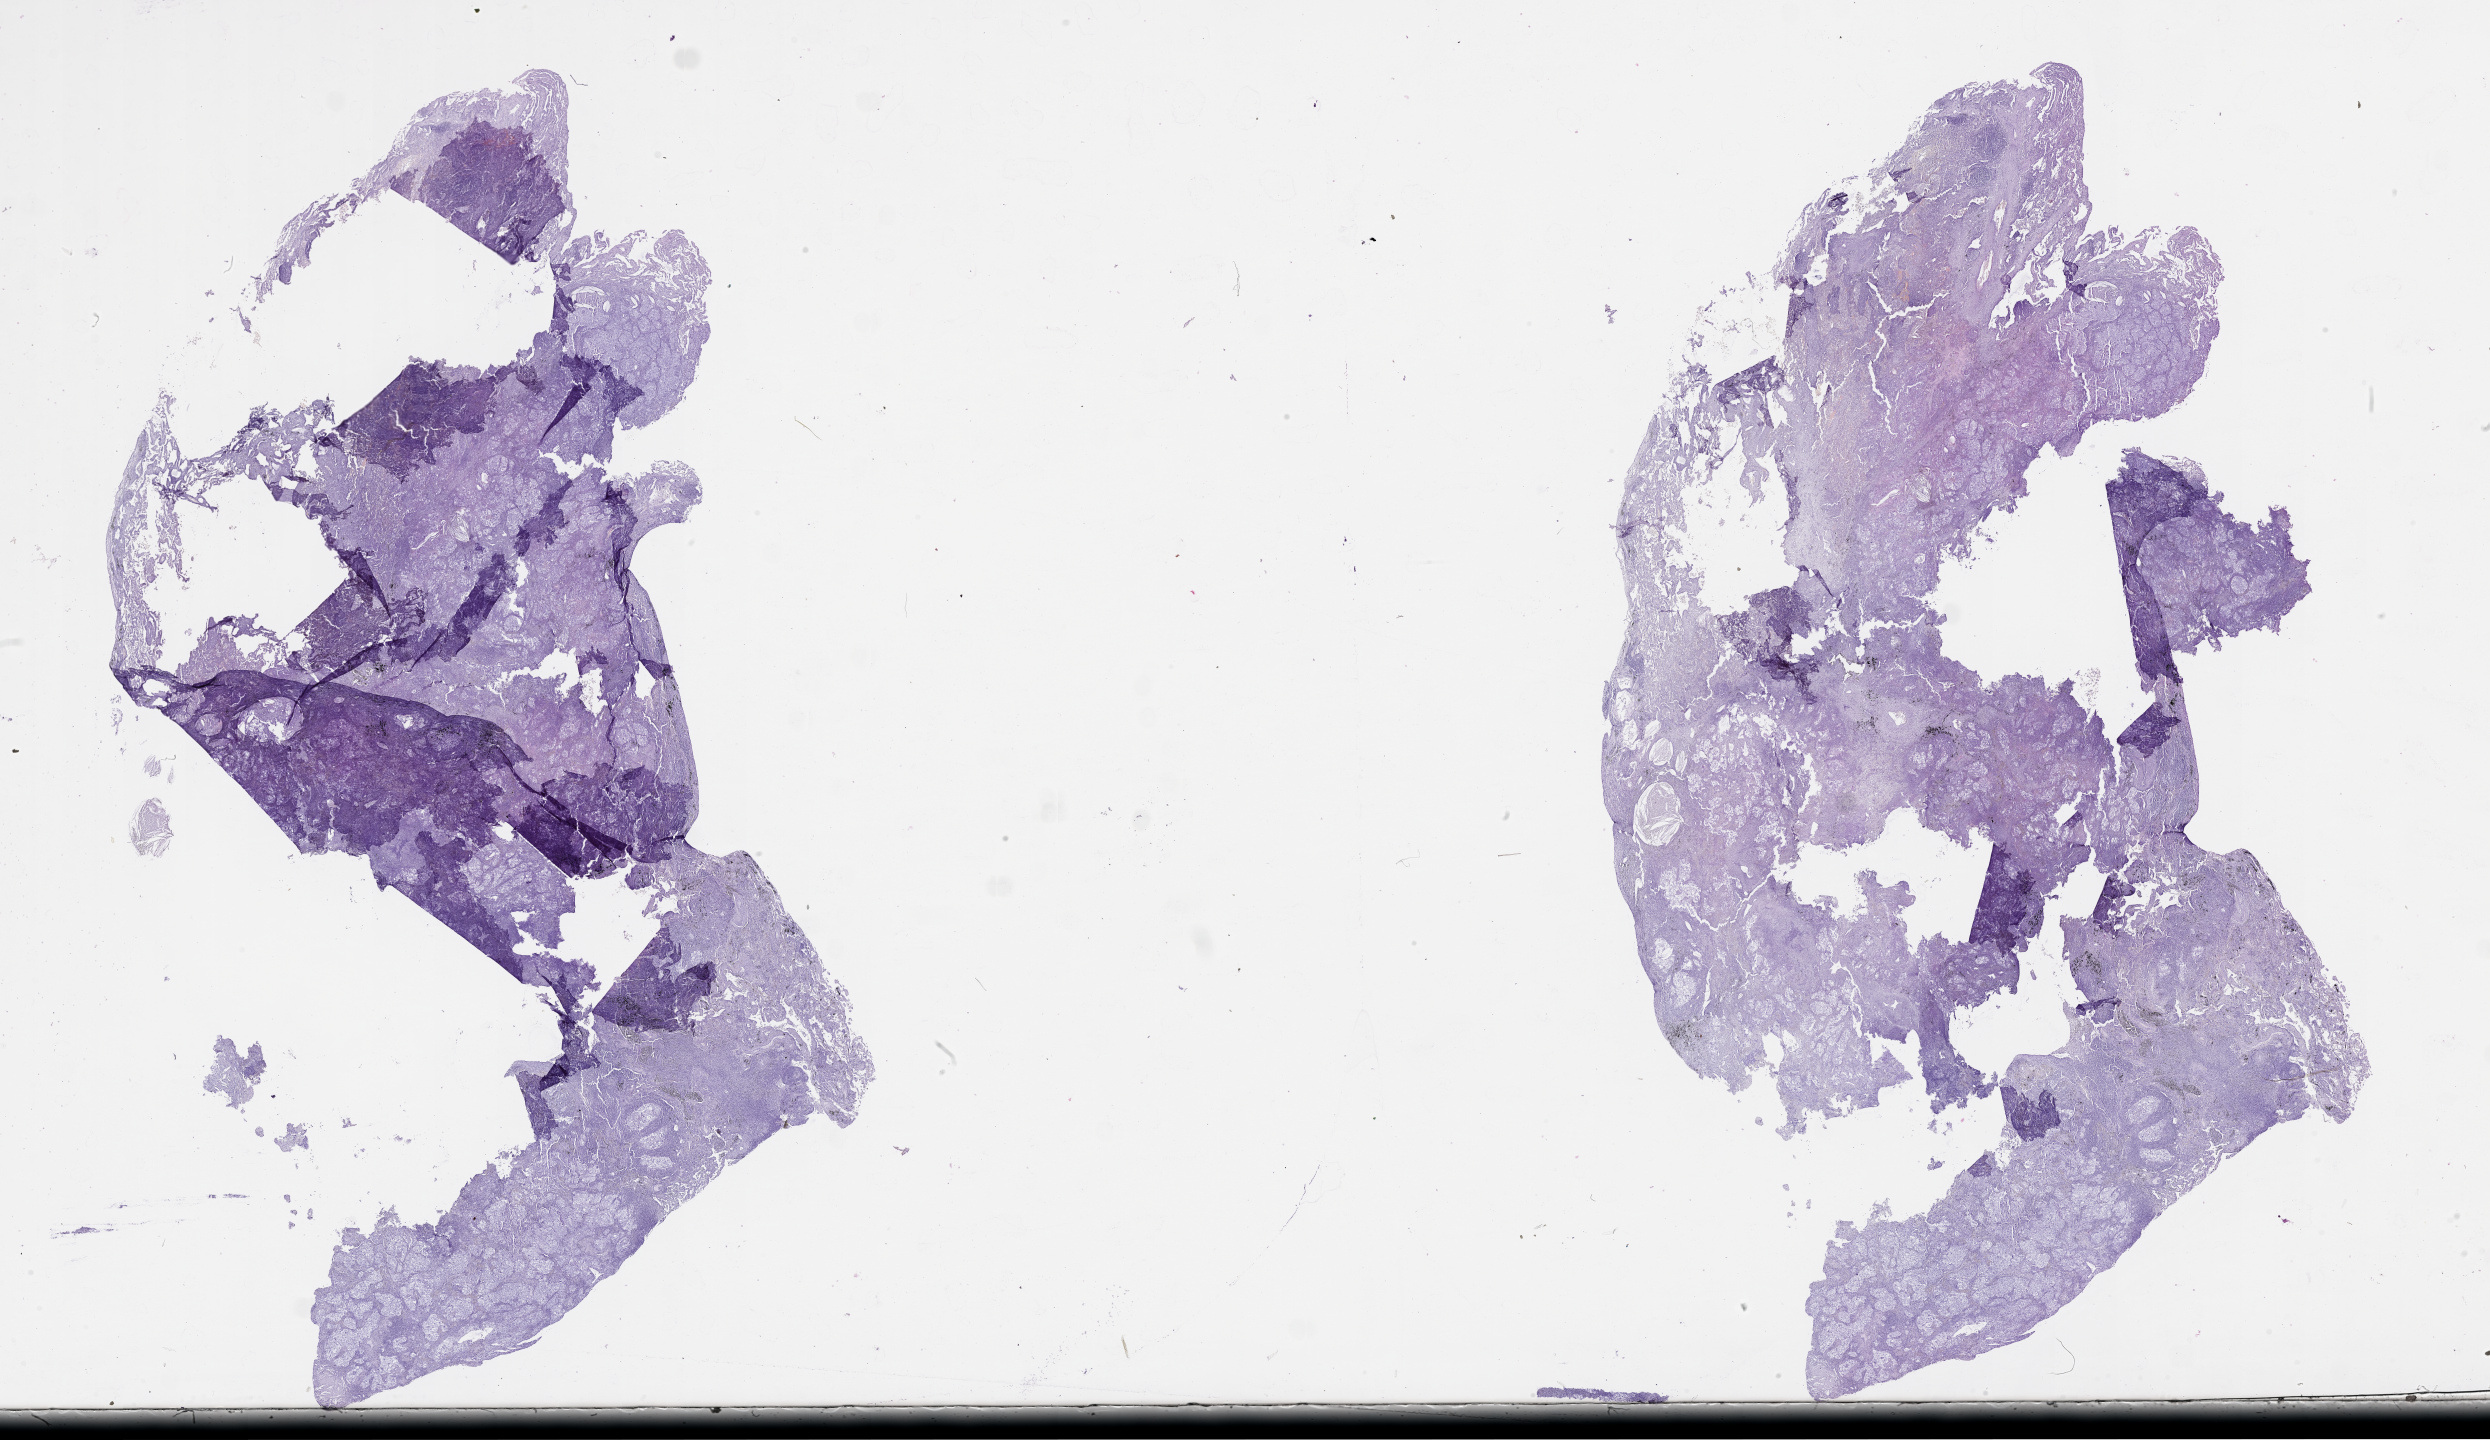
Hematoxylin and eosin (H&E) stained whole-slide image — low-resolution overview of the scanned area, about 40.1 x 23.2 mm (acquisition: 20x scan); tumour tissue sample, lung. Patient: male, age 68 years.
Patient diagnosis (cohort enrolment): squamous cell carcinoma (lung).